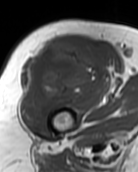
MRI of an extremity soft-tissue mass, one axial slice; position 71 of 99 along the scan axis; MR volume resampled by the dataset authors to the PET/CT grid (not the native acquisition matrix); 3.27 mm slice thickness; 138 × 172 image matrix, field of view 135 × 168 mm. Female patient. From the clinical record (not read from this slice): histological type: pleiomorphic undifferentiated sarcoma; grade: high; site of the primary tumour: right quadricep.
Outlined on this slice (expert contour drawn on MRI and transferred to this co-registered scan by the dataset authors):
- gross tumour volume including surrounding oedema: bounding box (x1, y1, x2, y2) in pixels: (21, 41, 102, 122)
- gross tumour volume (mass): (21, 41, 102, 122)